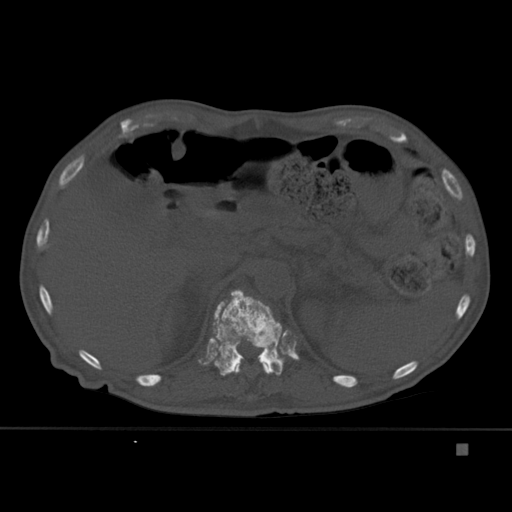
CT including the spine, one axial slice; position 204 of 451 along the scan axis; bone window (W 1800 / L 400 HU); 512 × 512 image matrix, field of view 378 × 378 mm. Patient: male, 75 years. Case-level facts recorded for this patient, not image findings: primary cancer: prostate.
Outlined on this slice (semi-automatic segmentation, software-assisted and operator-edited):
- T11 vertebra: bounding box (x1, y1, x2, y2) in pixels: (232, 358, 272, 374)
- T12 vertebra: (210, 289, 285, 376)